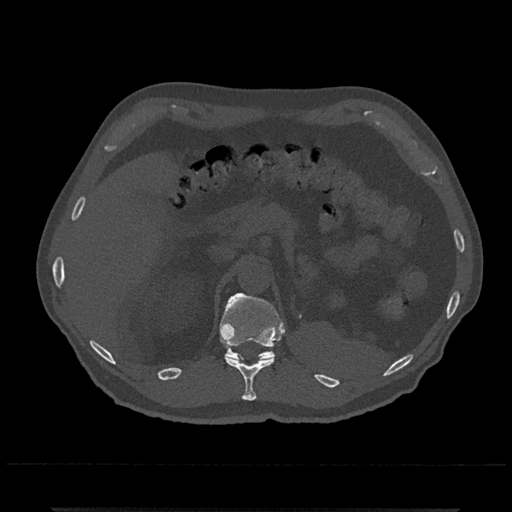
CT including the spine, one axial slice. Position 461 of 797 along the scan axis. Bone window (W 1800 / L 400 HU). 0.5 mm slice thickness. 512 × 512 image matrix, field of view 393 × 393 mm. Male patient, age 67 years. From the clinical record (not read from this slice): primary cancer: prostate.
Annotated regions visible in this slice (semi-automatically segmented with operator editing):
- T11 vertebra: bounding box (x1, y1, x2, y2) in pixels: (225, 356, 275, 401)
- T12 vertebra: (219, 293, 285, 361)